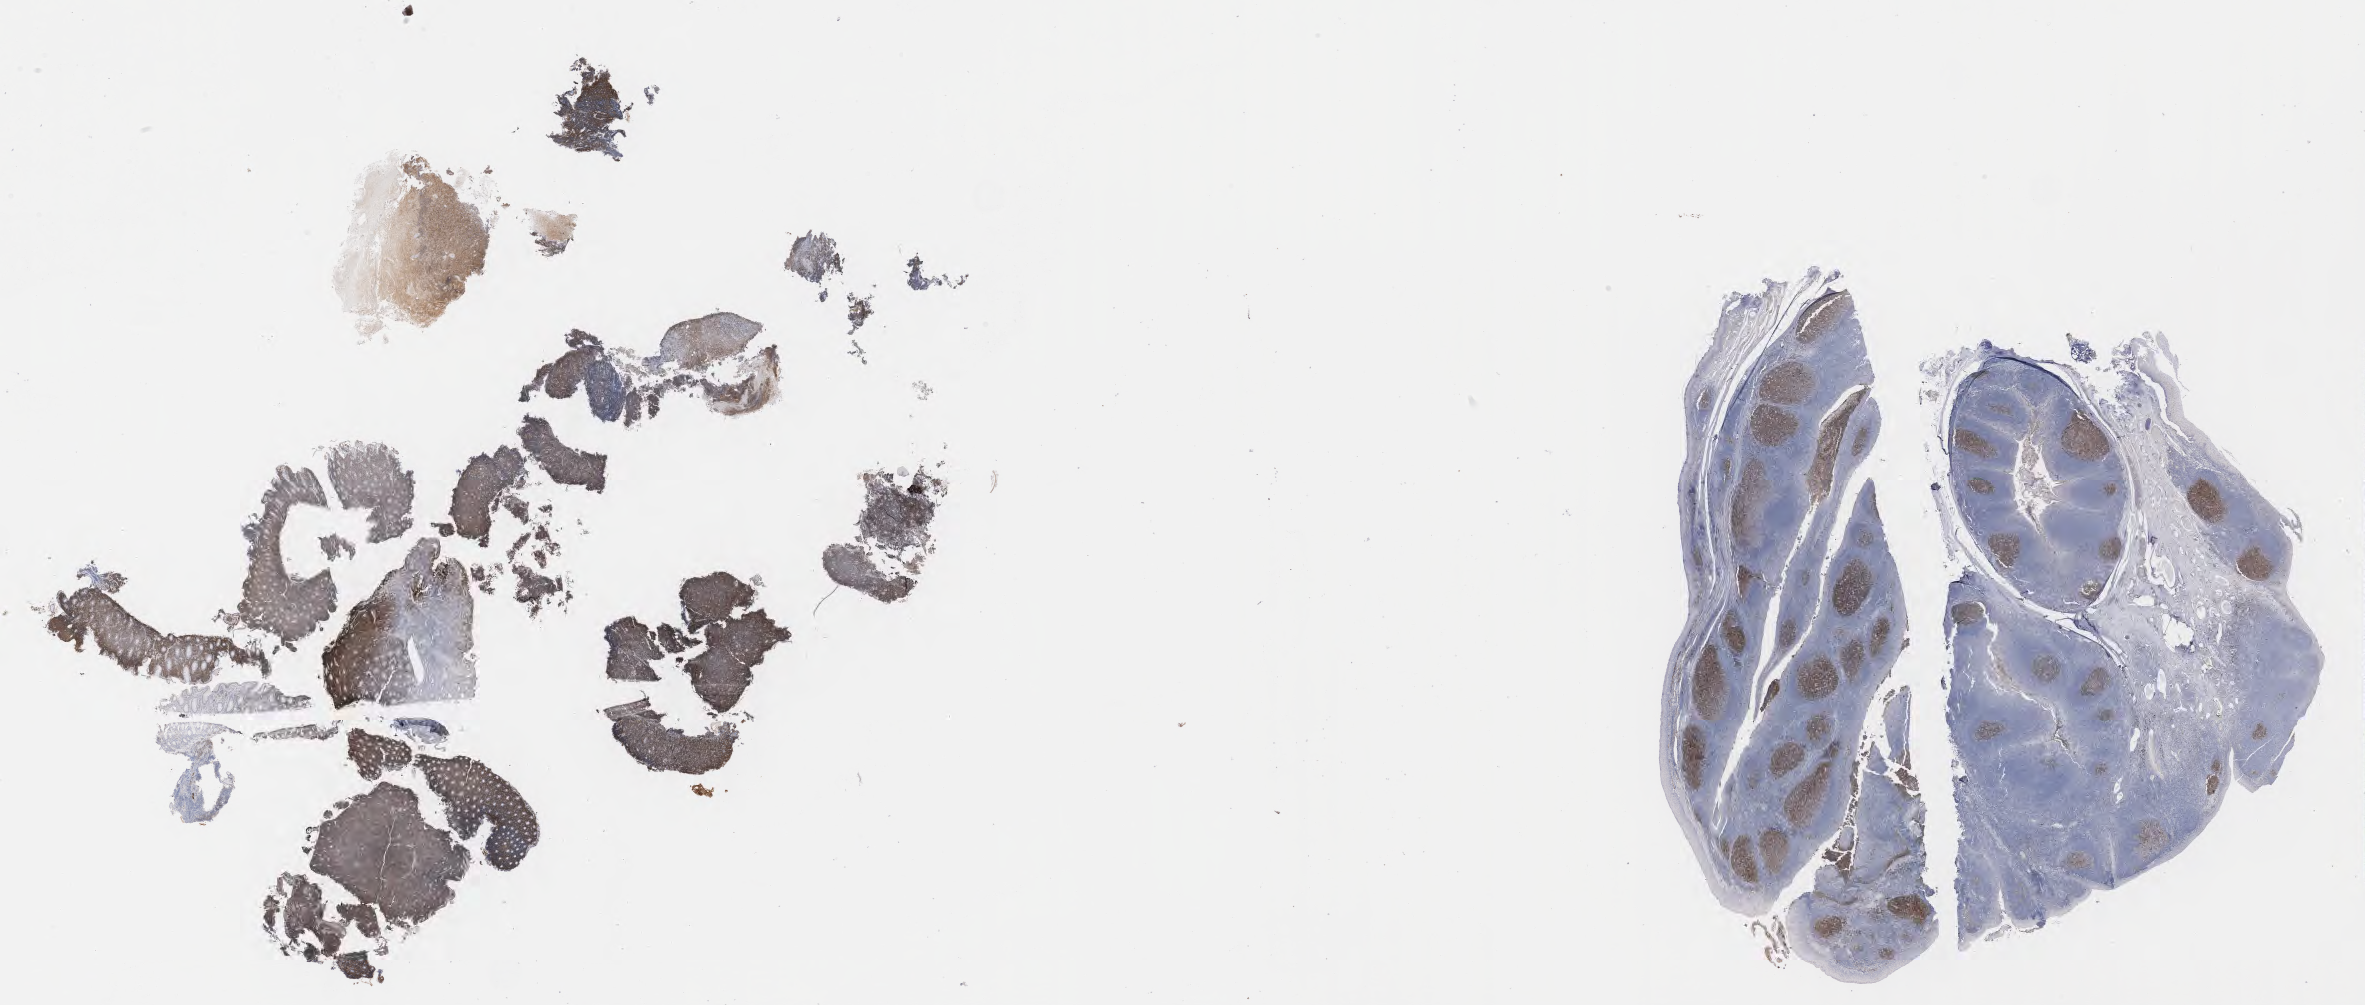
Whole-slide image, immunohistochemical stain for CD10, low-resolution overview of the scanned area, about 38.2 x 16.2 mm. Specimen: tumor tissue. Male patient, 56 years old.
Histologic diagnosis: Burkitt lymphoma, NOS.